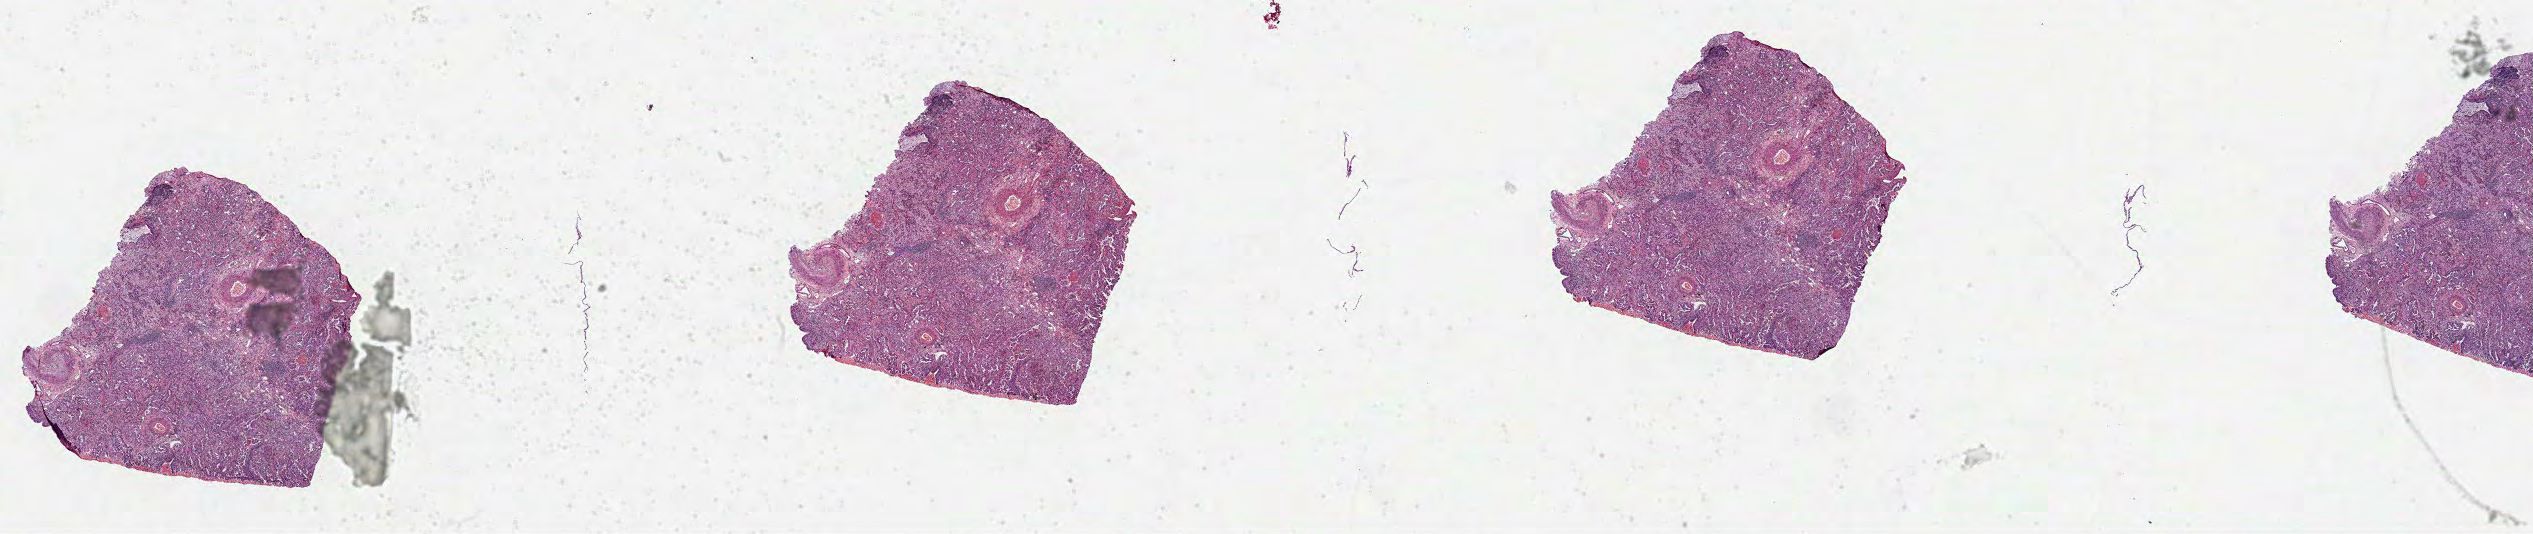
Digitized H&E tissue section (whole slide), a low-resolution overview of the entire scanned area, about 40.9 x 8.6 mm (from a 40x scan). Formalin-fixed paraffin-embedded (FFPE) diagnostic section. Primary tumour sample from the lung. Female, age 67 years at initial diagnosis.
* histologic diagnosis: Adenocarcinoma, NOS (upper lobe, lung)
* AJCC pathologic stage: IA (7th edition)